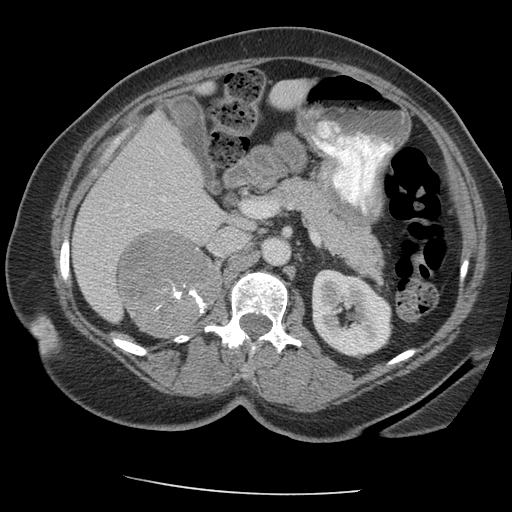
Contrast-enhanced abdominal CT, one axial slice; slice 119 of 163 in the series (ordered by position); reconstruction kernel STANDARD; 140 kVp; intravenous contrast given; soft-tissue window (W 400 / L 40 HU); 2.5 mm slice thickness; 512 × 512 image matrix, field of view 360 × 360 mm. Female patient, age 70 years. From the clinical record (not read from this slice): diagnosis: adrenocortical carcinoma; tumour side: right adrenal; tumour size at pathology: 9.5 cm; Ki-67 index: 5 %; stage (as recorded): 2.
Annotated regions visible in this slice (semi-automatic segmentation, software-assisted and operator-edited):
- mass: box from (x=119, y=230) to (x=219, y=335) px